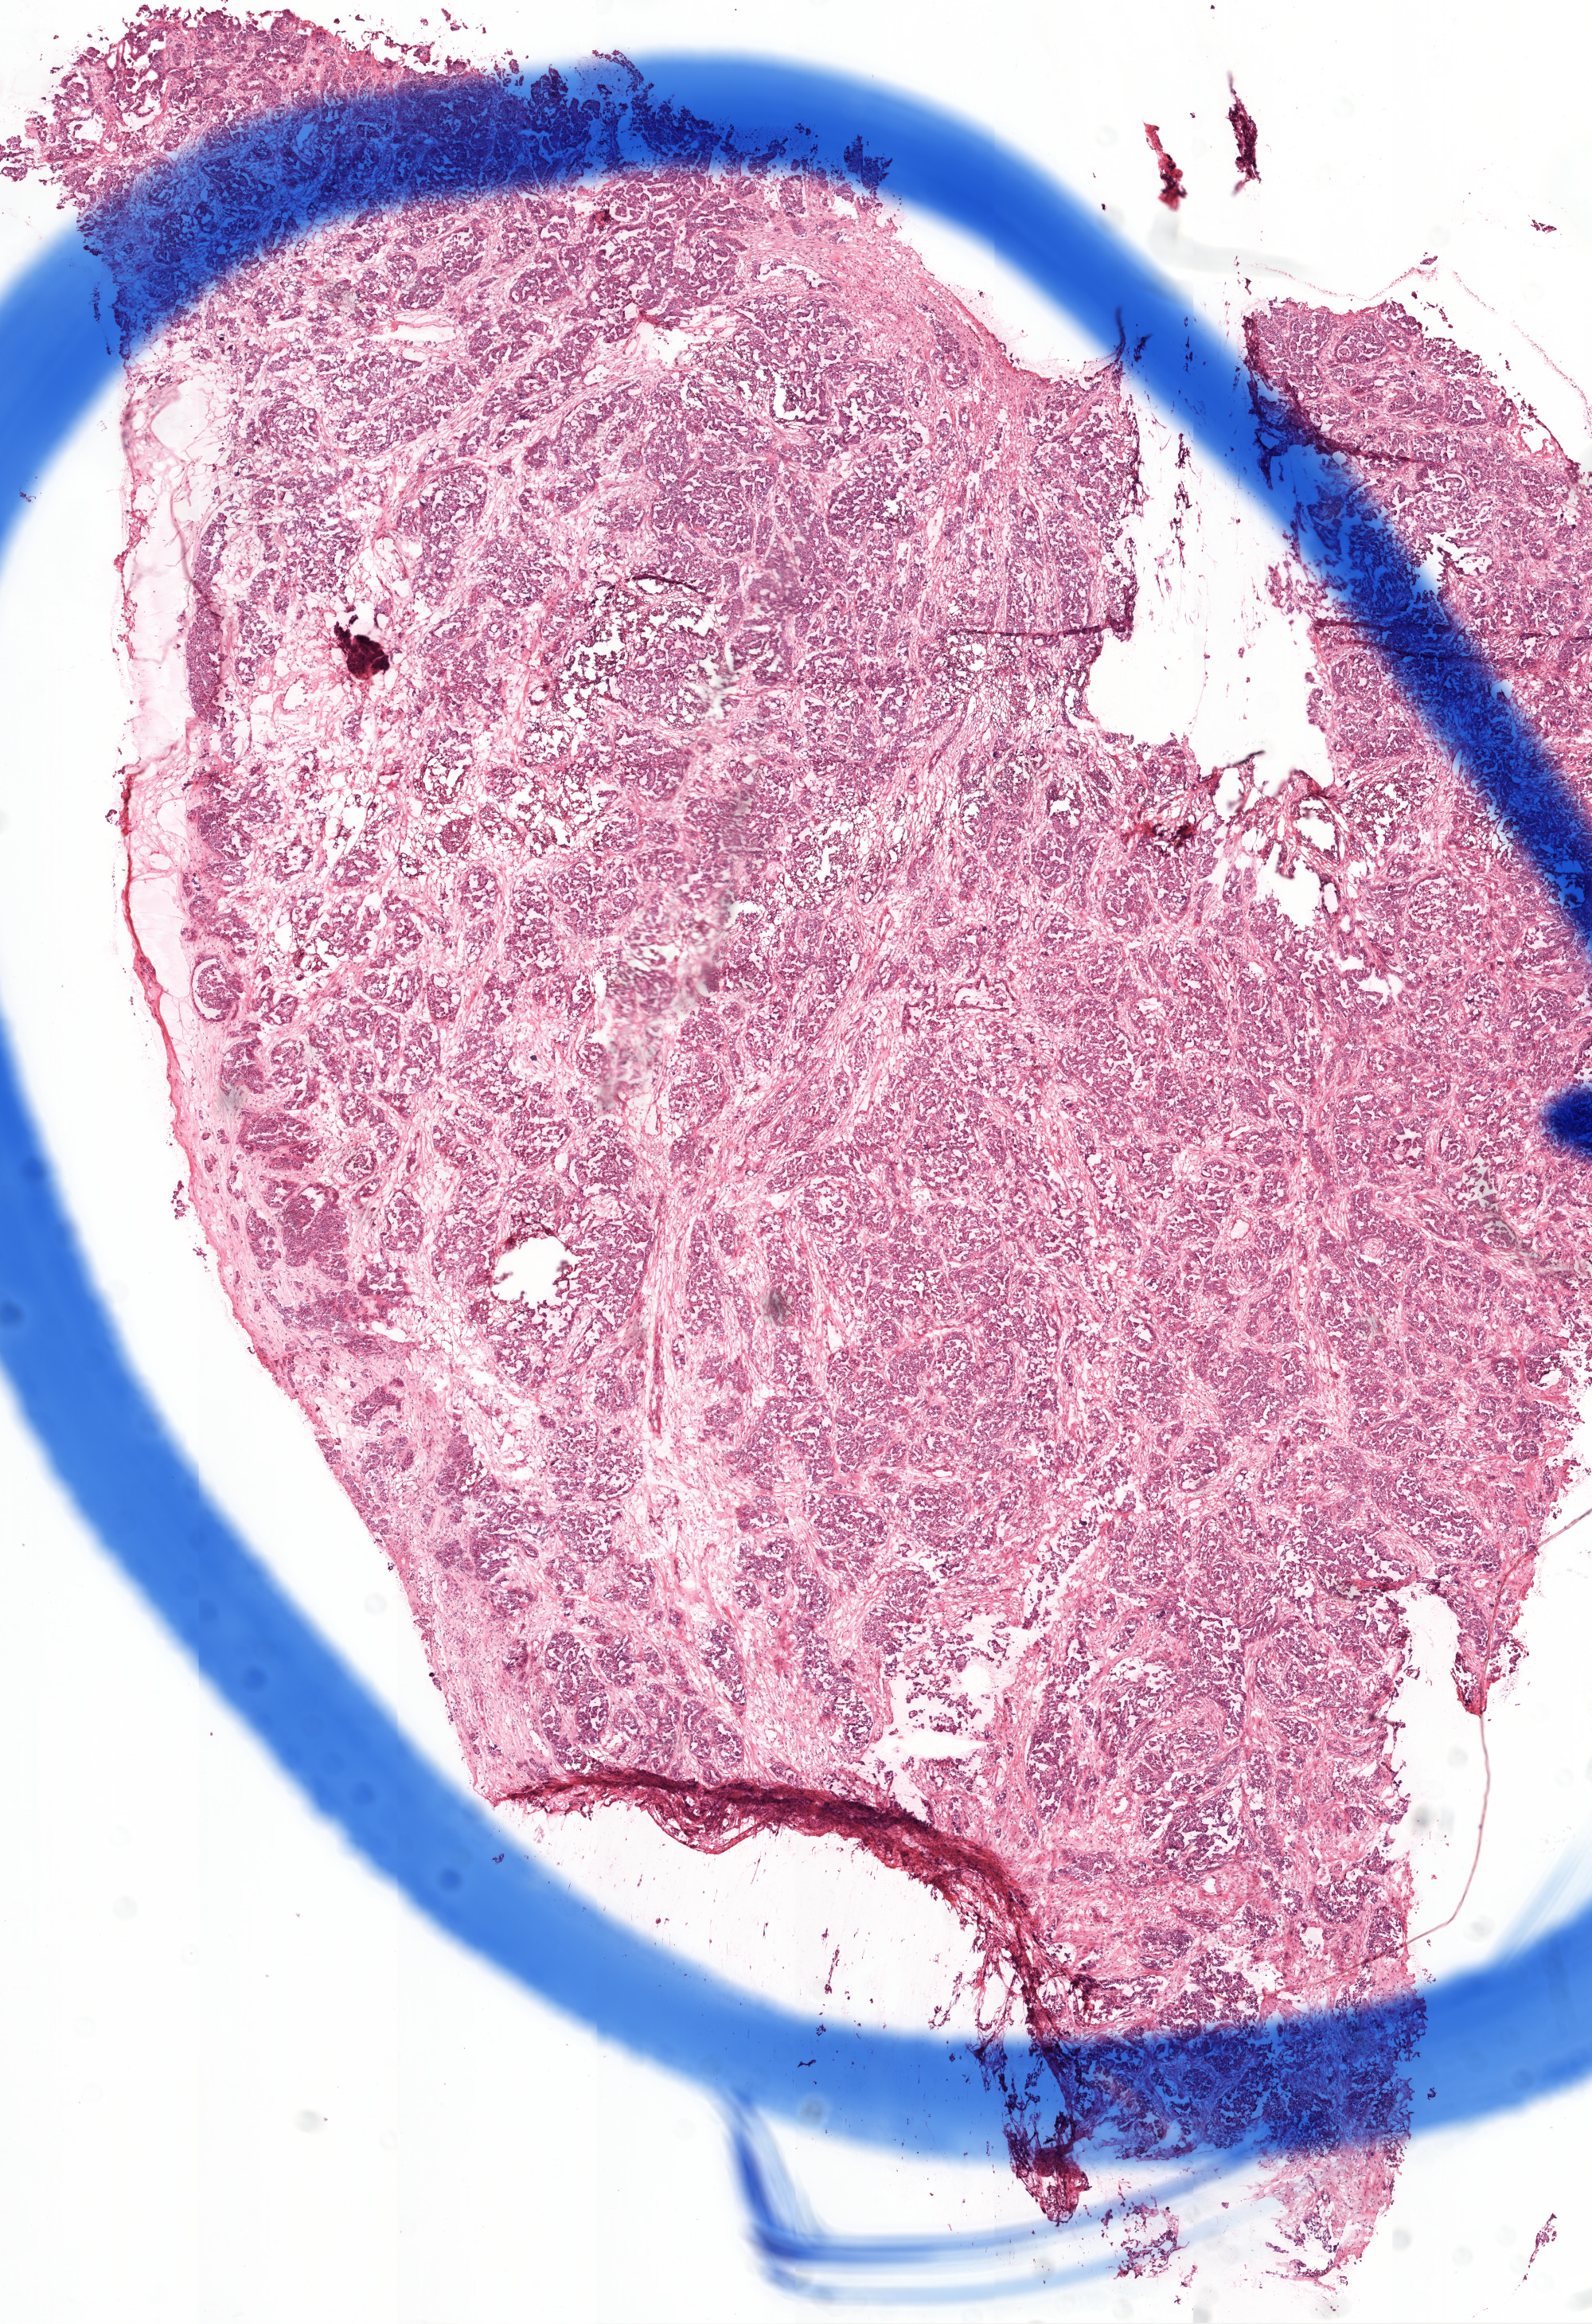
H&E whole-slide image — whole scanned area (about 8.0 x 11.7 mm) shown as a low-resolution overview; frozen section from the top of the tissue portion; sample: primary tumour, ovary. Female, age 71 years at initial diagnosis. Histologic grade: G3 (poorly differentiated). Slide review estimates, as recorded: tumour cells 98%, tumour nuclei 85%, normal cells 0%, stromal cells 0%, necrosis 2%. Inflammatory infiltration, as recorded: lymphocyte infiltration 5%.
FIGO stage: IIIC. Diagnosis: Serous cystadenocarcinoma, NOS.